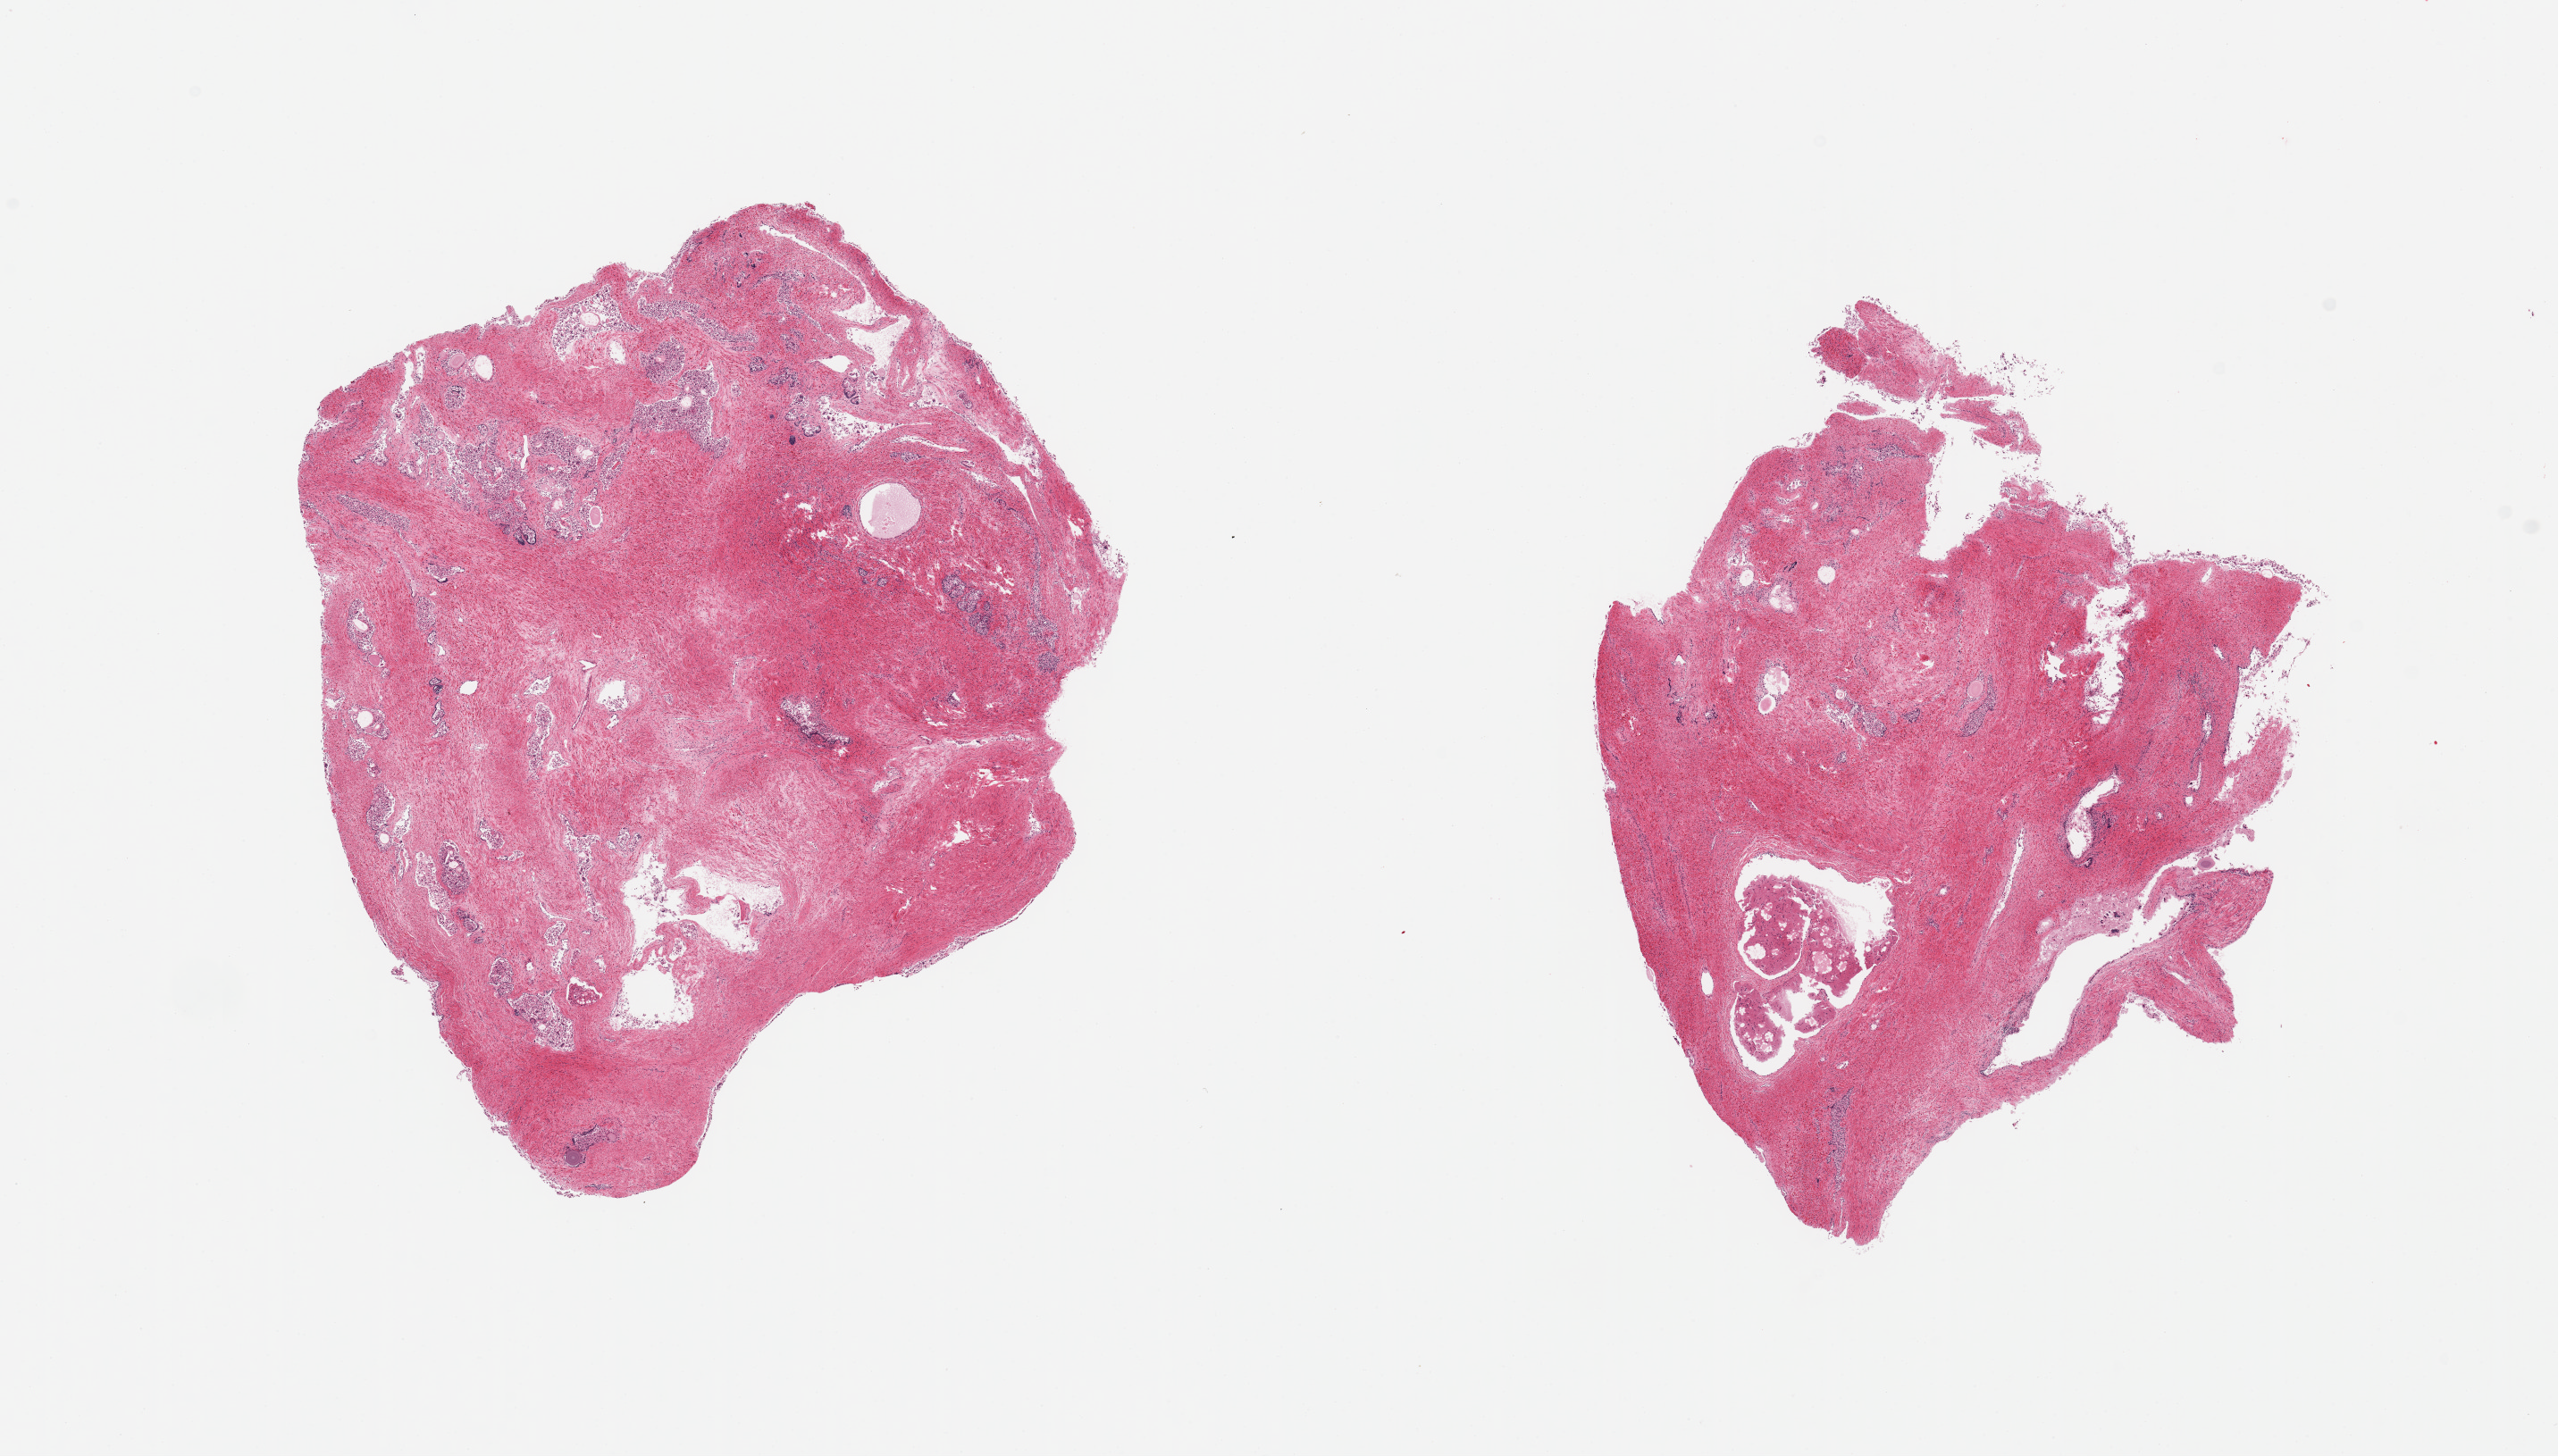
Whole-slide image, haematoxylin and eosin stain — whole scanned area (about 22.6 x 12.9 mm, slide scanned at 20x) shown as a low-resolution overview, PAXgene-fixed, paraffin-embedded tissue, section of prostate (target tissue), donor tissue sample.
Review note (as recorded): 2 pieces: fibromuscular stroma with dispersed glands with sloughed epithelium, apparent cyst.